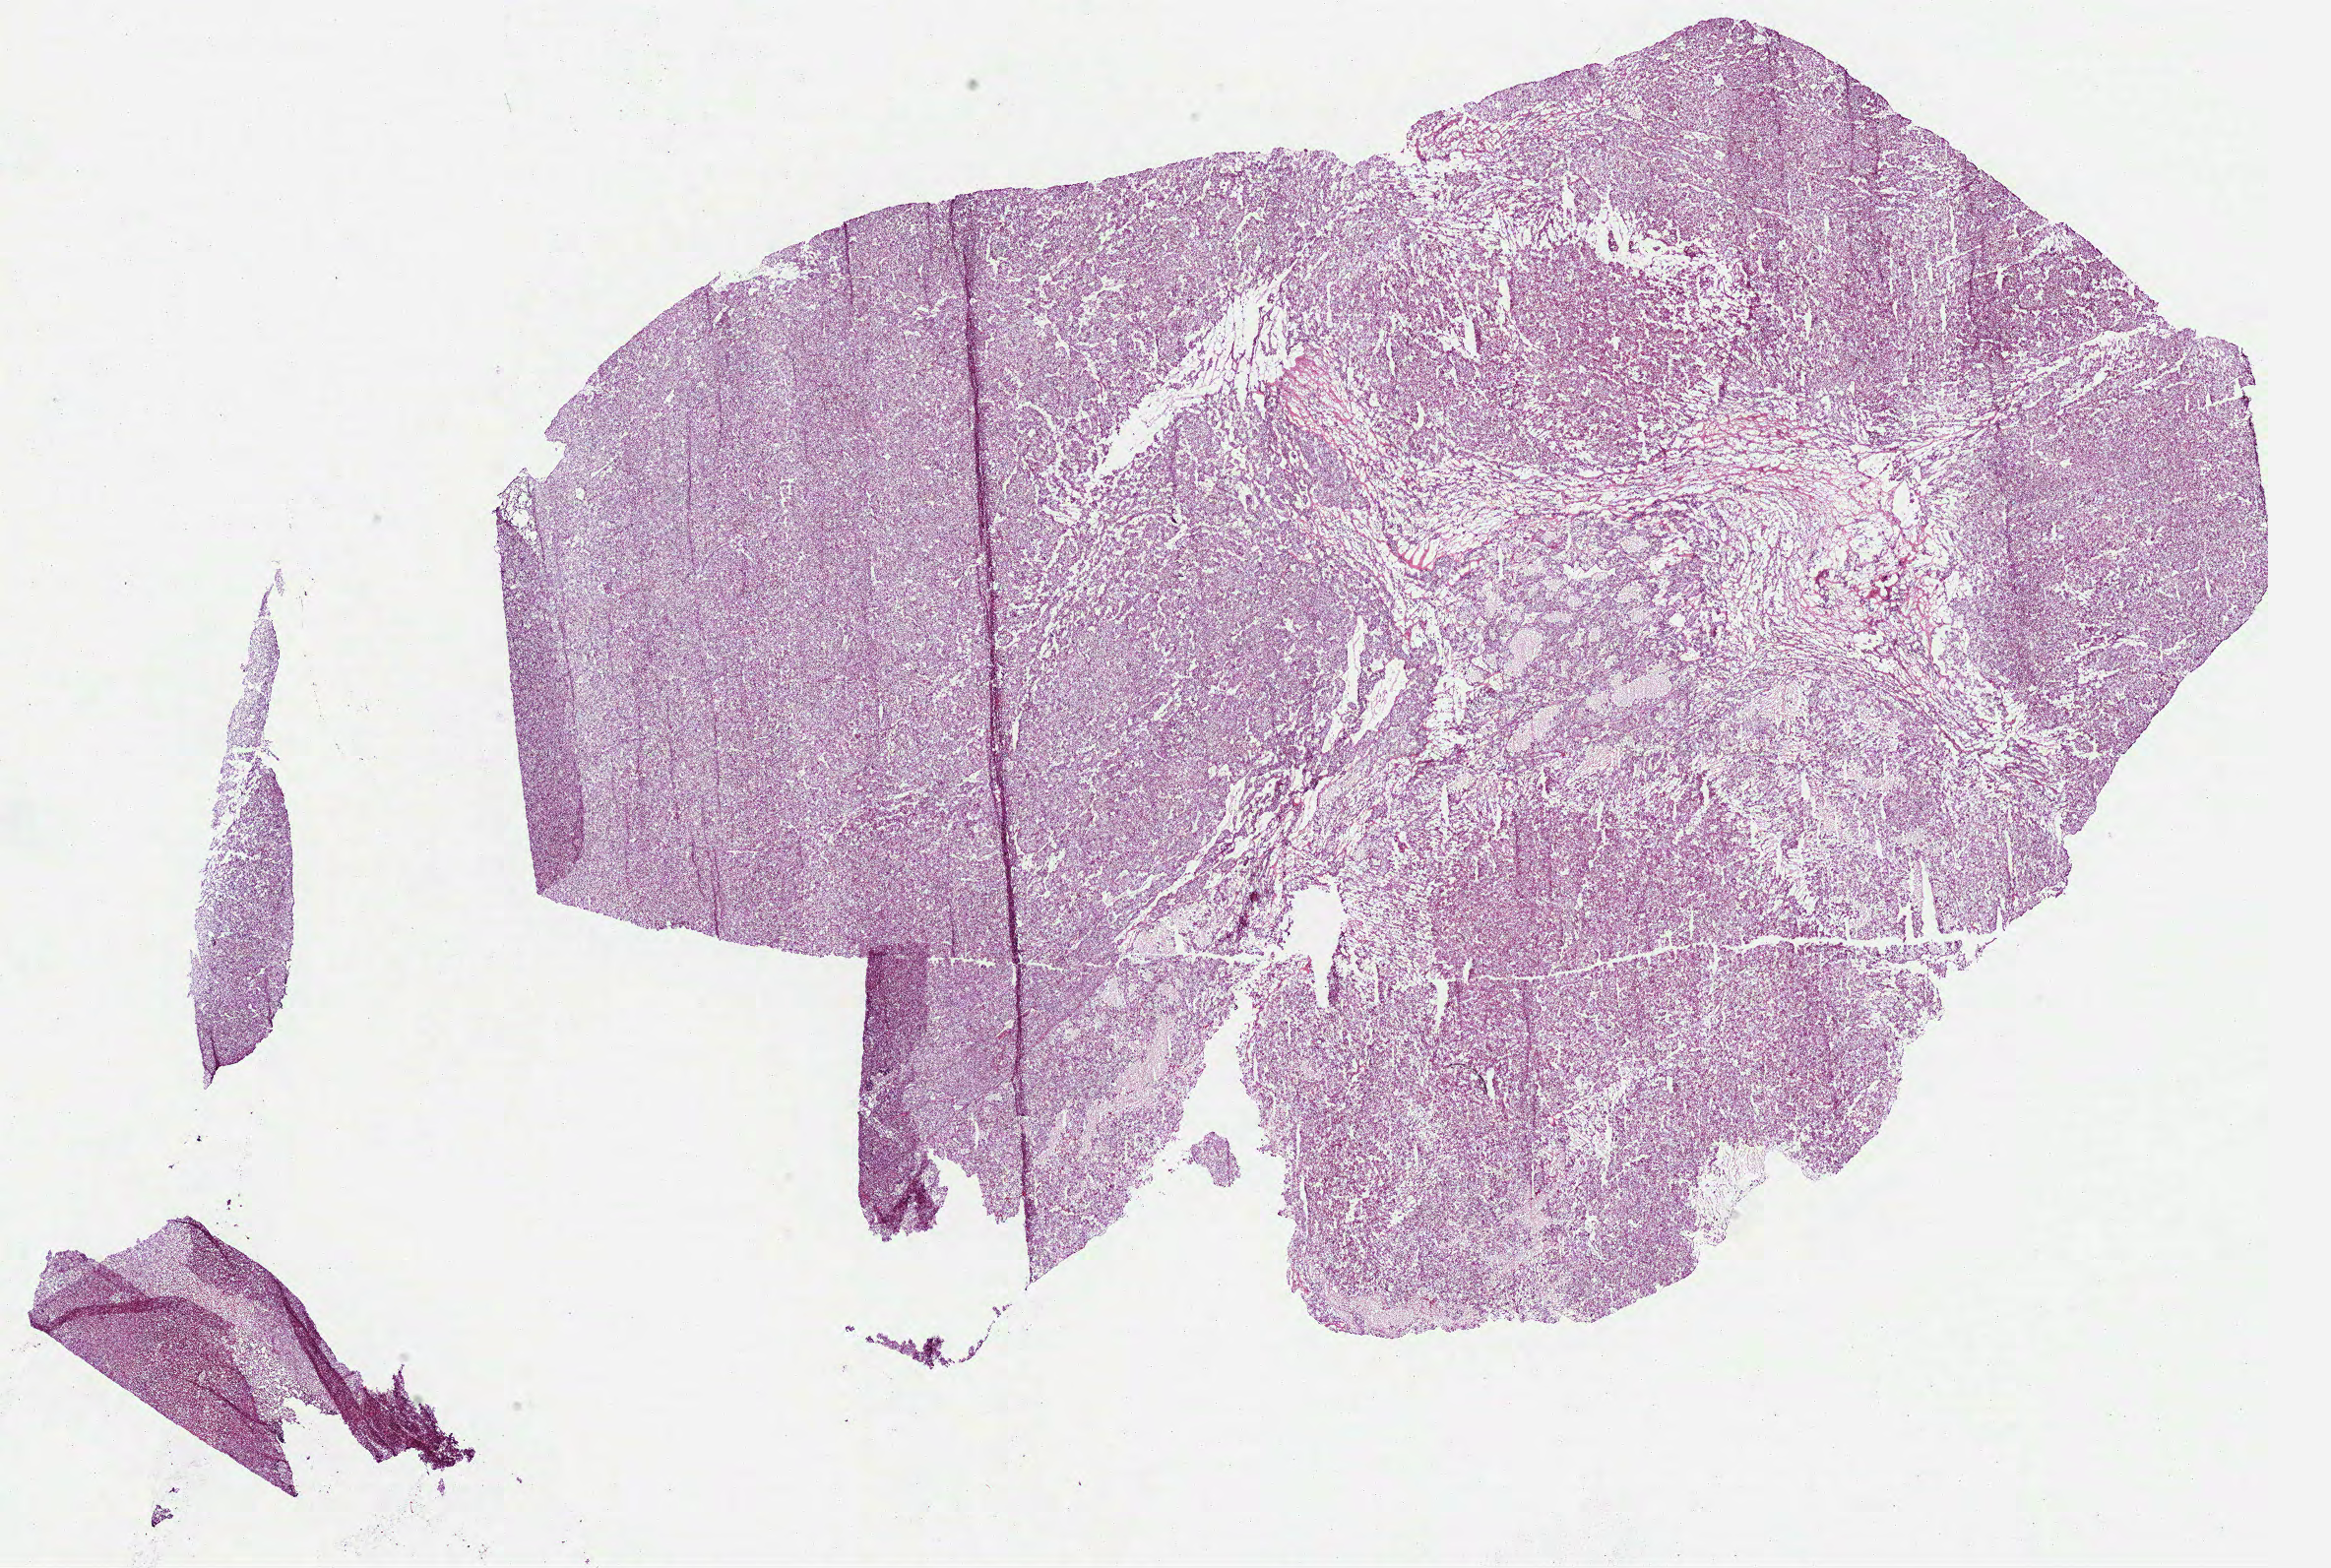
Whole-slide histology image, H&E, shown as a low-resolution overview of the whole scanned area (about 19.1 x 12.8 mm, from a 40x scan), frozen section from the bottom of the tissue portion, sample: primary tumour, kidney. Male patient; age at initial diagnosis 50 years. Slide review estimates, as recorded: tumour cells 100%, tumour nuclei 95%, normal cells 0%, stromal cells 0%, necrosis 0%. Infiltration values recorded for this section: lymphocyte infiltration 0%, monocyte infiltration 0%, neutrophil infiltration 0%.
AJCC pathologic stage: IV. Diagnosis: Renal cell carcinoma, chromophobe type. TNM: T3a NX M1.